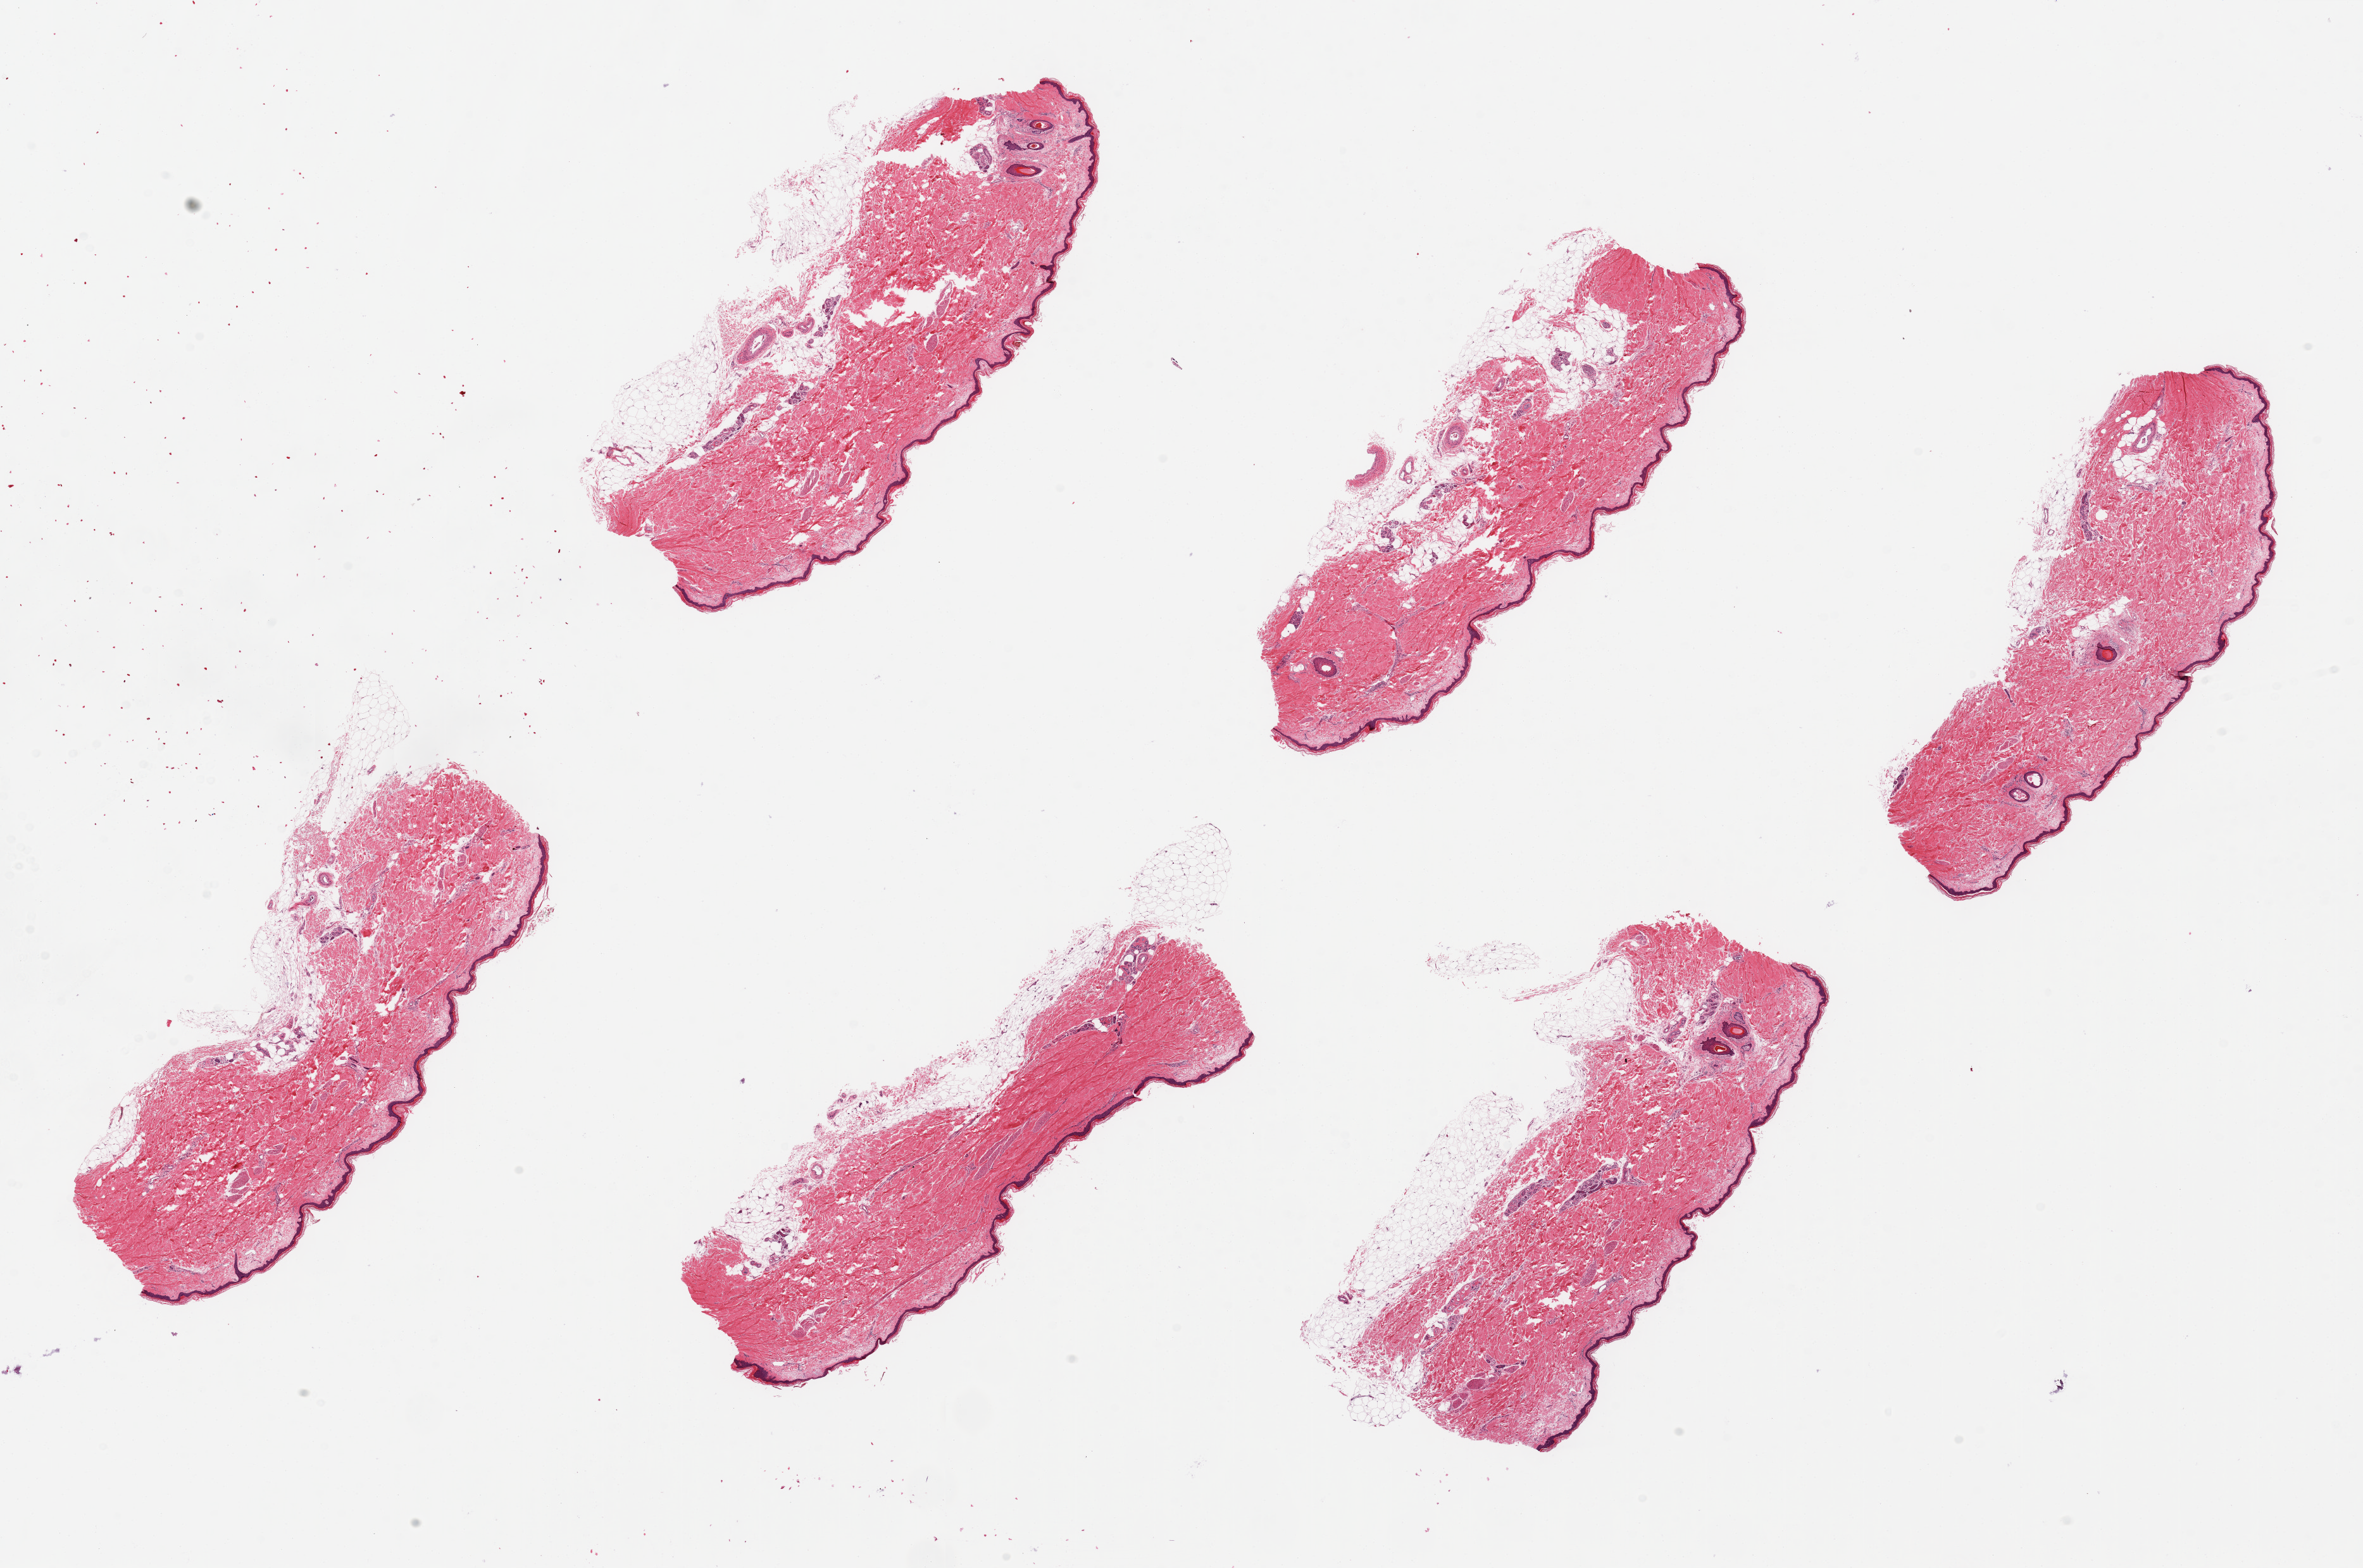
Whole-slide image, haematoxylin and eosin stain, brightfield, a low-resolution overview of the entire scanned area, about 29.5 x 19.6 mm (acquisition: 20x scan). PAXgene-fixed paraffin-embedded (PFPE) section. Sampled site (target tissue): skin of lower leg. Donor tissue sample. Donor sex: male.
• reviewer comment on this tissue sample: 6 pieces, ~ 7x.25mm -squamous epithelium is less than 2 % of thickness